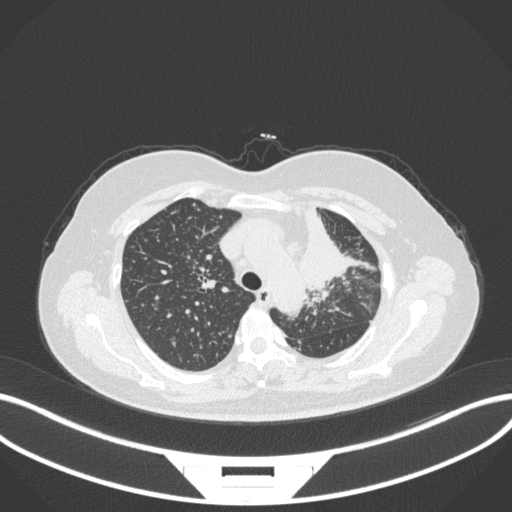
Chest CT, one axial slice. Position 249 of 348 along the scan axis. Reconstruction kernel B31f. 120 kVp. Lung window (W 1500 / L -600 HU). 1 mm slice thickness. 512 × 512 image matrix, field of view 400 × 400 mm. Female patient, age 49 years. From the clinical record (not read from this slice): clinical TNM (as recorded): T1c N0 M1.
Structures marked on this image (bounding box drawn by a radiologist):
- lung tumour (recorded histology: adenocarcinoma): bounding box <297,200,359,297> (left, top, right, bottom; pixels)